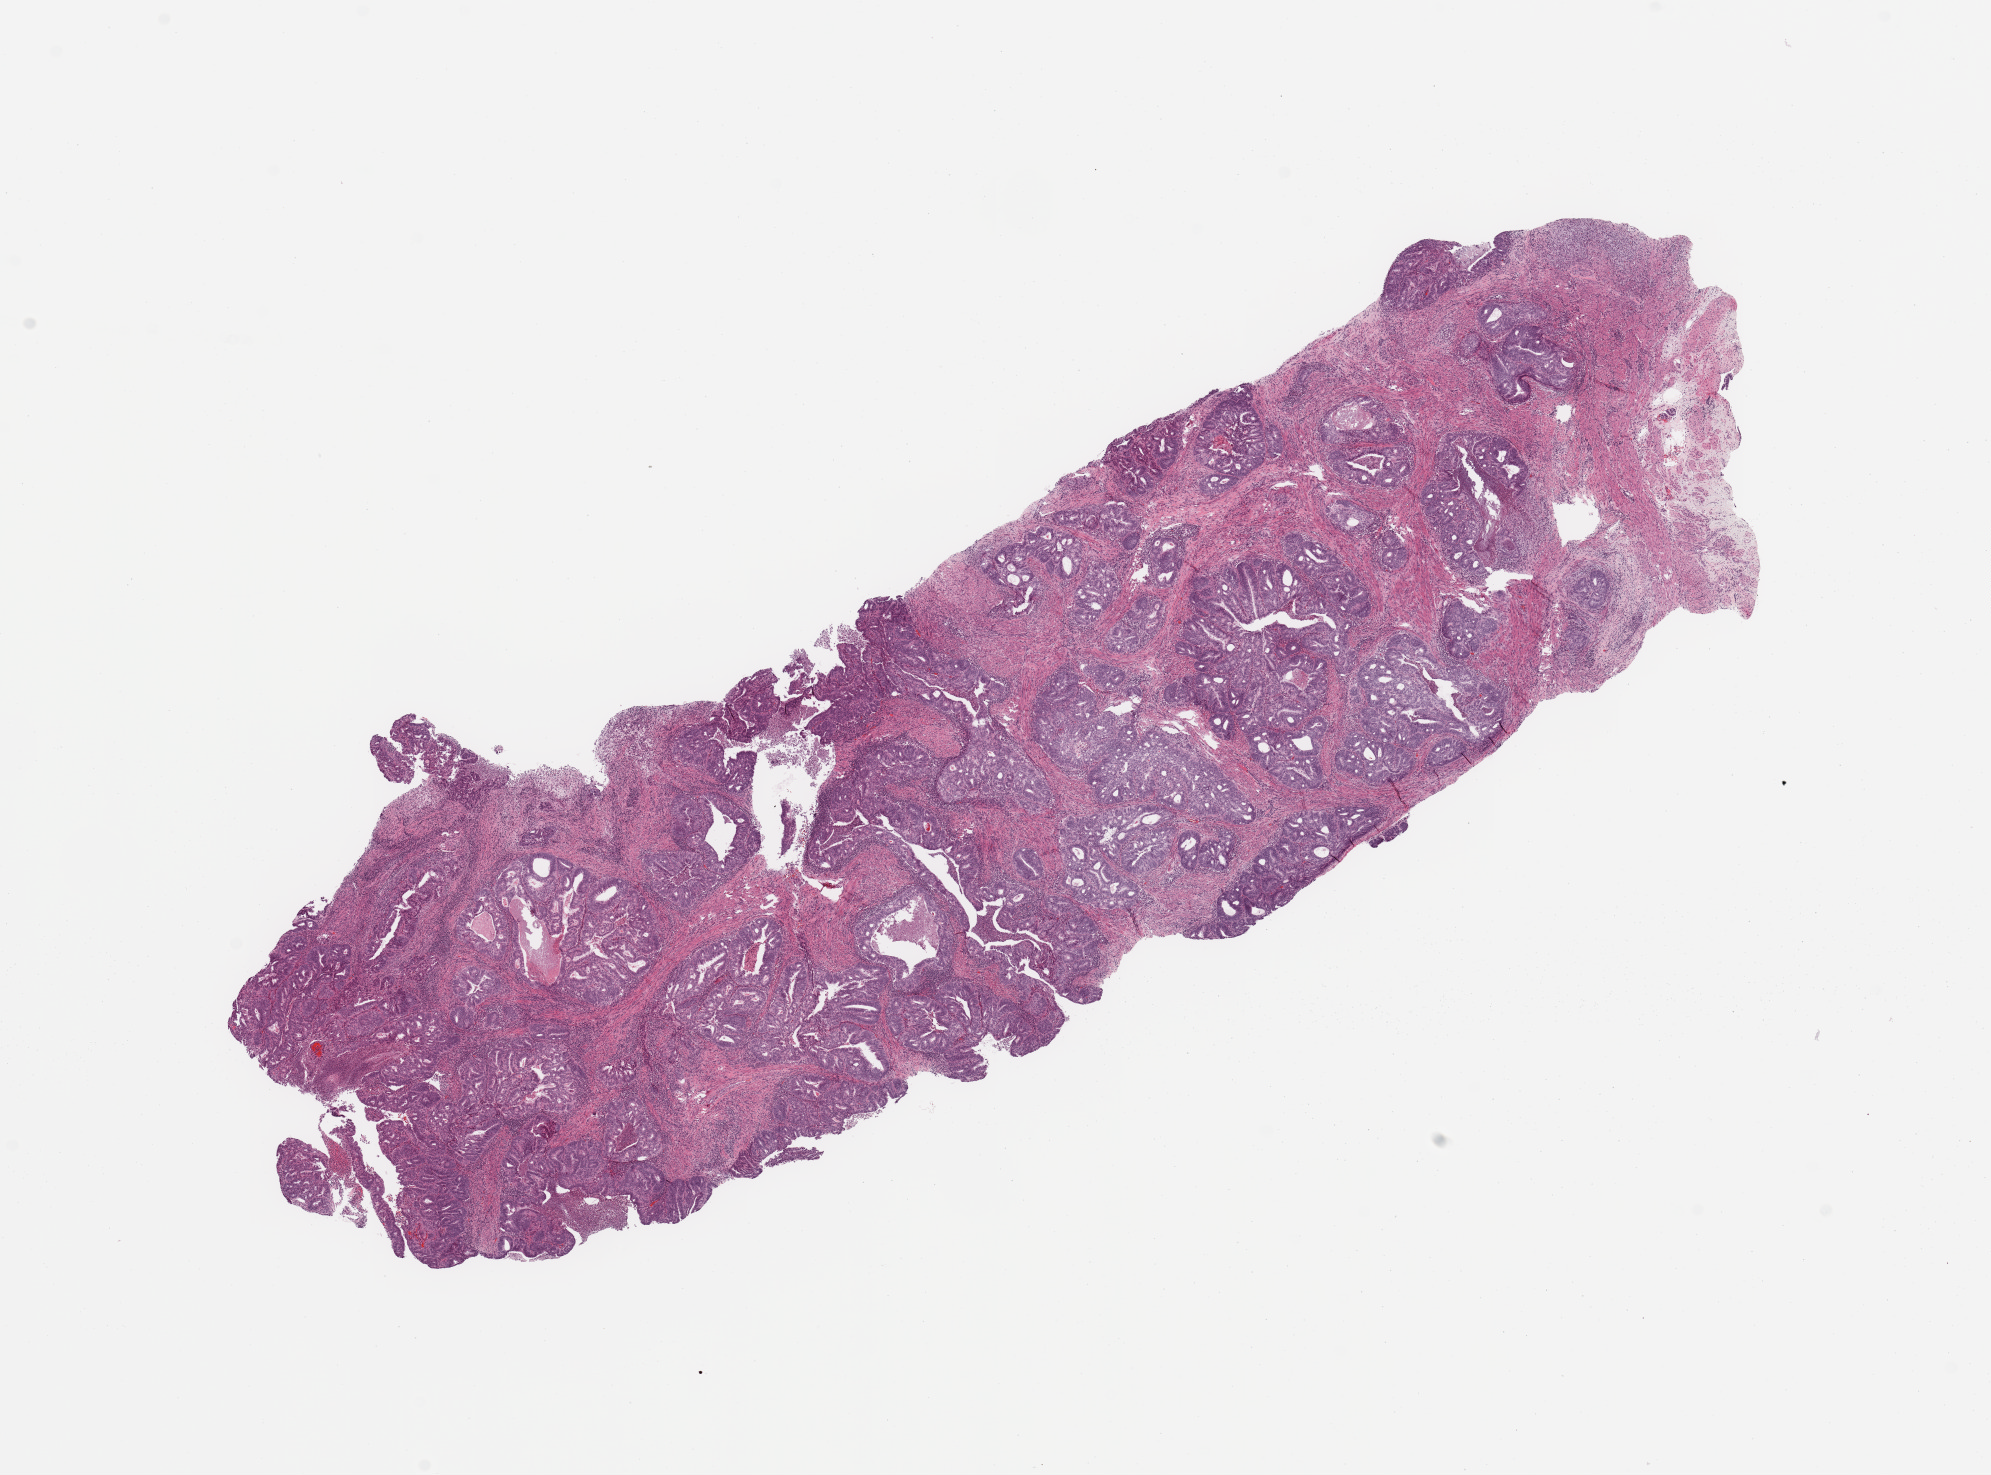
H&E-stained whole-slide image — shown as a low-resolution overview of the whole scanned area (about 15.8 x 11.7 mm); tumour tissue sample, sampled site: uterus. Patient: female, age 80 years. Histologic grade: G2 (moderately differentiated). Slide review estimates, as recorded: tumour nuclei 80%, necrosis 5%.
* AJCC pathologic stage: I
* primary tumour site (as recorded): posterior endometrium
* diagnosis: Endometrioid adenocarcinoma, NOS